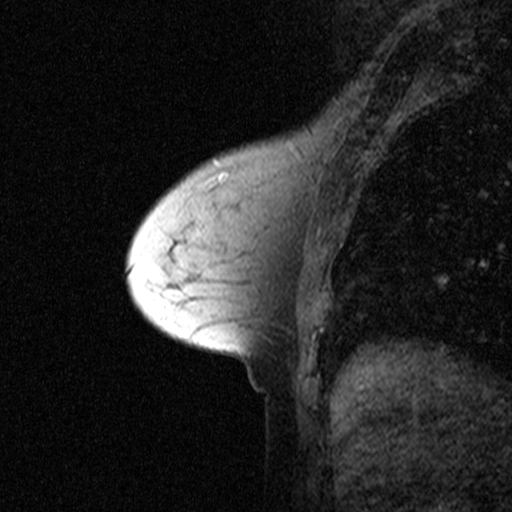
Breast MRI (dynamic contrast-enhanced), one sagittal slice; dynamic contrast-enhanced study with each time point stored as its own series, time point 2 of 3 at this slice position (early post-contrast, ordered by acquisition time); 1.5 T; TE 4.5 ms, TR 11 ms; 512 × 512 image matrix, field of view 200 × 200 mm. Patient: female, 53 years. From the clinical record (not read from this slice): setting: breast cancer imaged before/during neoadjuvant chemotherapy; receptor status: HR-positive, HER2-negative.
Annotated regions visible in this slice (semi-automatic segmentation, software-assisted and operator-edited):
- analysis volume of interest (the breast-tissue region the enhancement analysis was run in; not a lesion): bounding box <170,150,277,273> (left, top, right, bottom; pixels)
- tumour enhancement mask (voxels above the 90 % enhancement threshold inside the analysis volume of interest): <223,176,228,180>